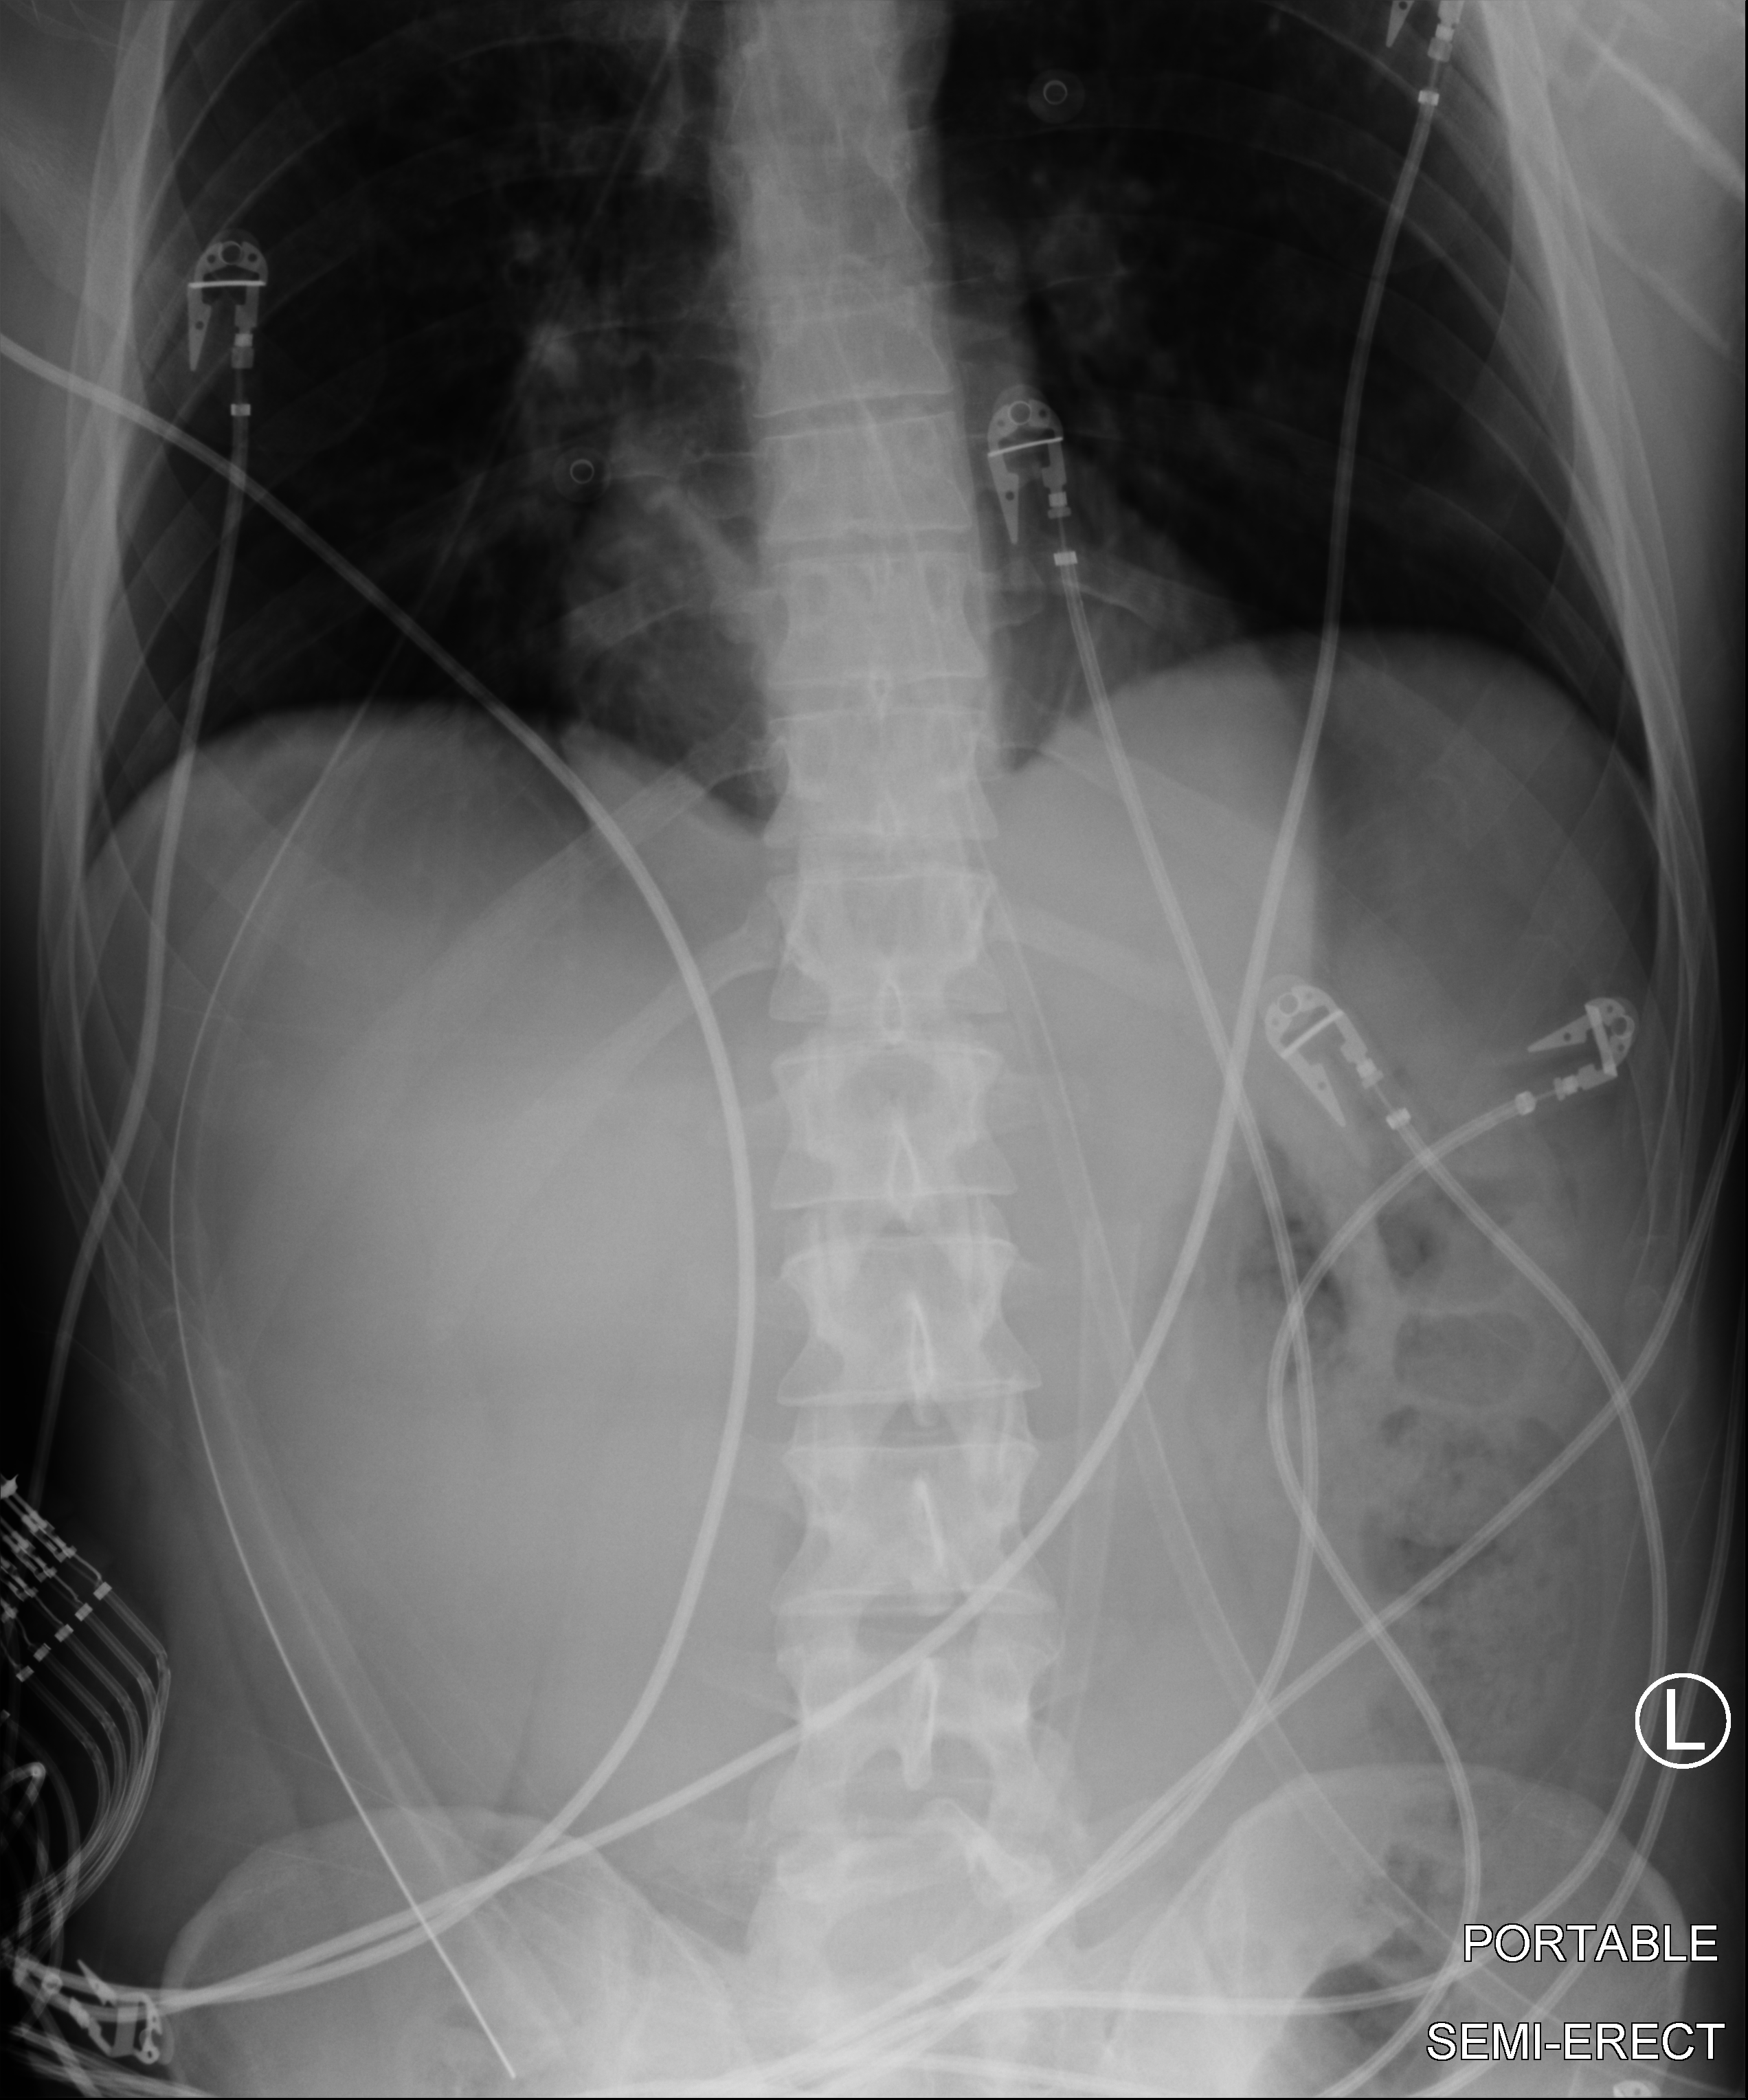
Chest X-ray (portable), anteroposterior (AP) projection. Male patient hospitalised with COVID-19, age 18–59 years.
Admission-level facts for this patient (not findings on this image; timing relative to this image not recorded):
- mechanically ventilated during this hospital stay: yes